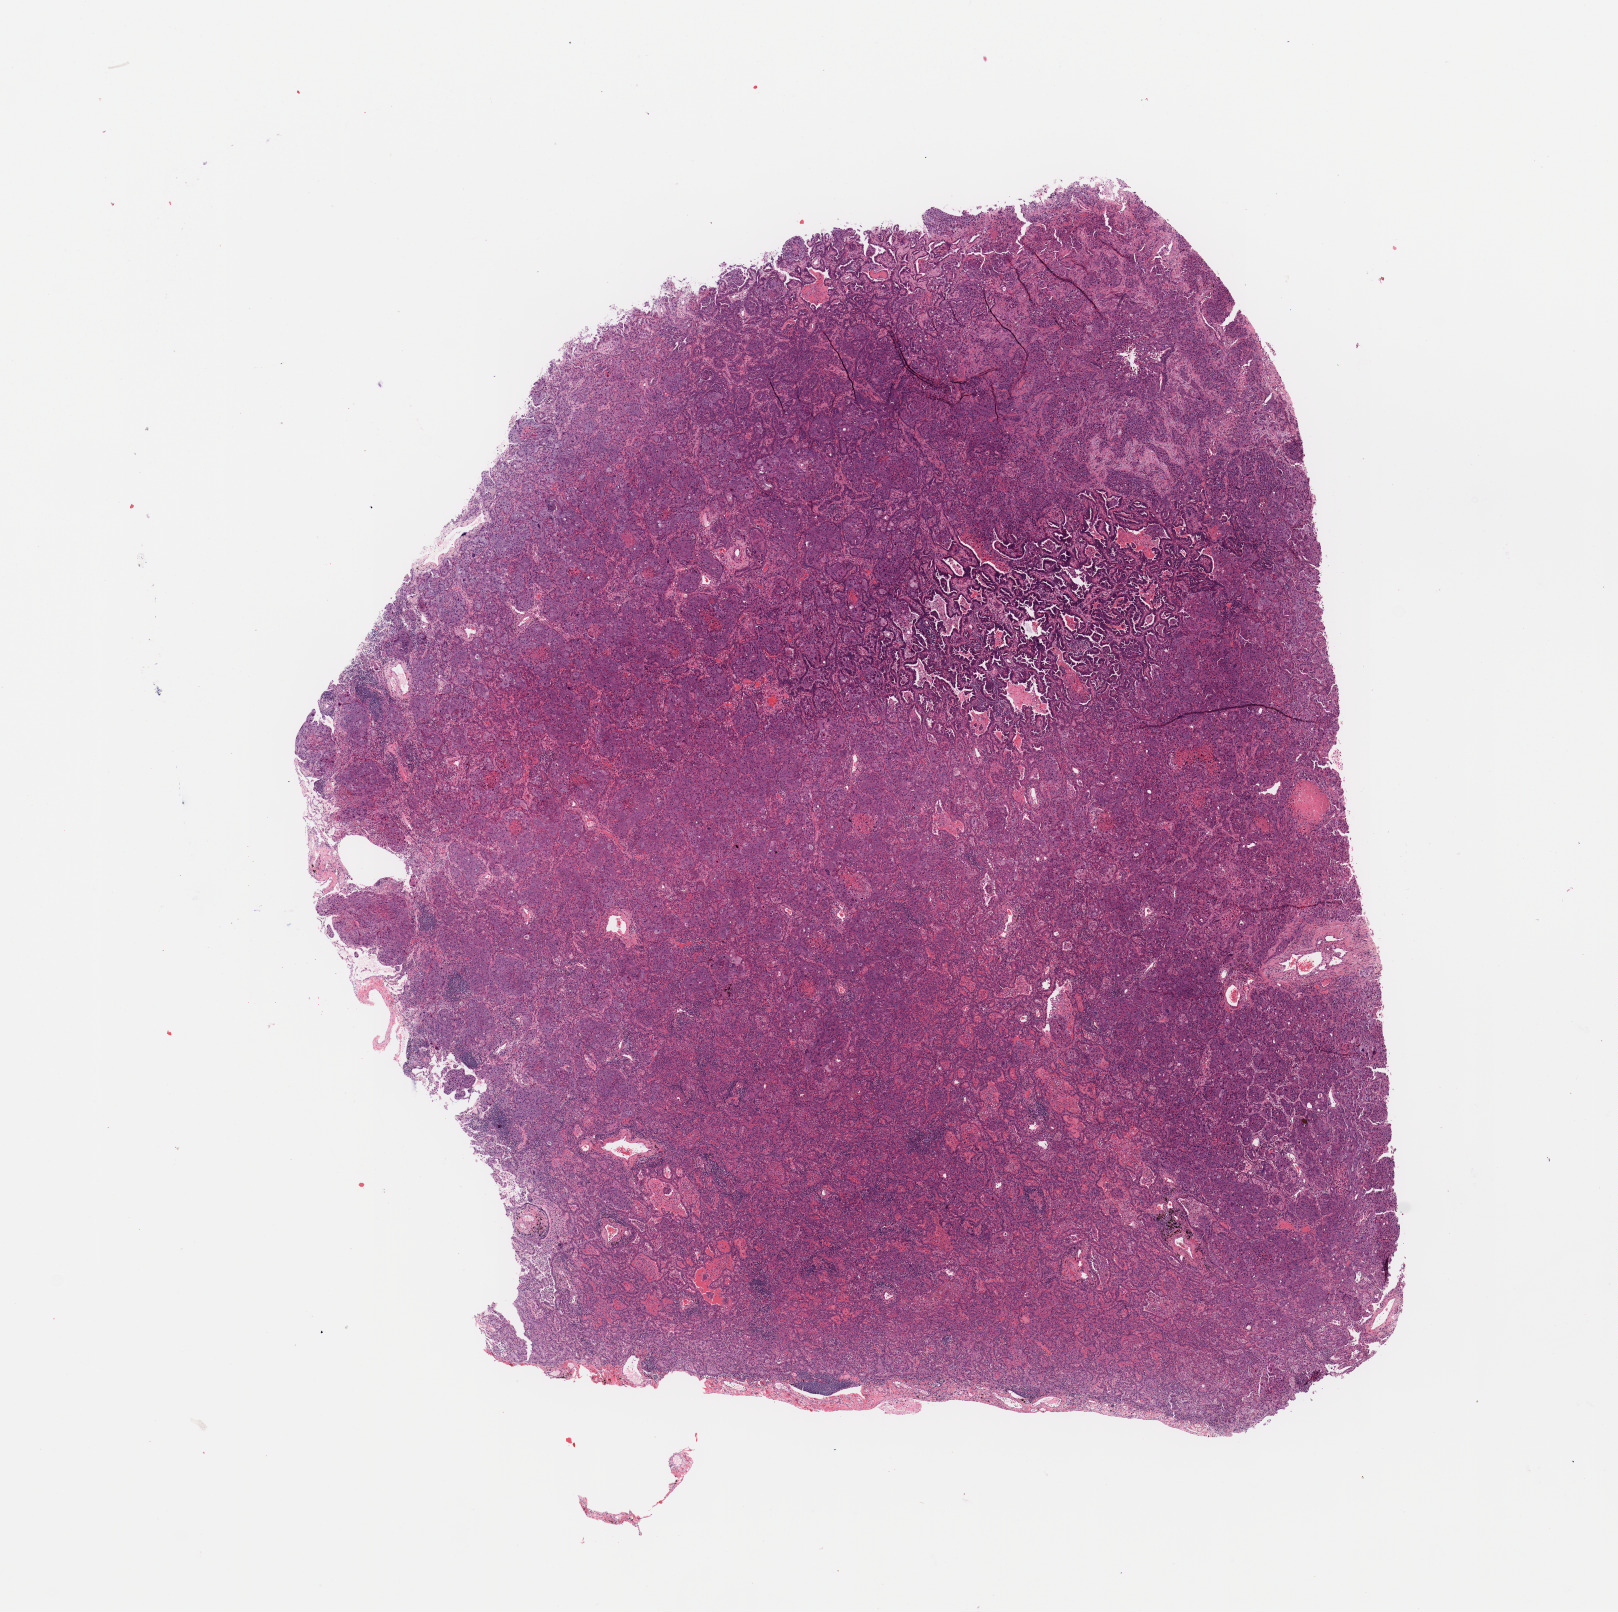
Digitized Hematoxylin and eosin (H&E) stained tissue section (whole slide) — whole scanned area (about 12.8 x 12.7 mm, slide scanned at 20x) shown as a low-resolution overview. Tumour tissue sample, sampled site: lung. Female, 53 y/o. Histologic grade: G3 (poorly differentiated). Slide review estimates, as recorded: tumour nuclei 80%, necrosis 3%.
• AJCC pathologic stage: IIIA
• primary tumour site (as recorded): right lower lobe
• histologic diagnosis: Adenocarcinoma, NOS